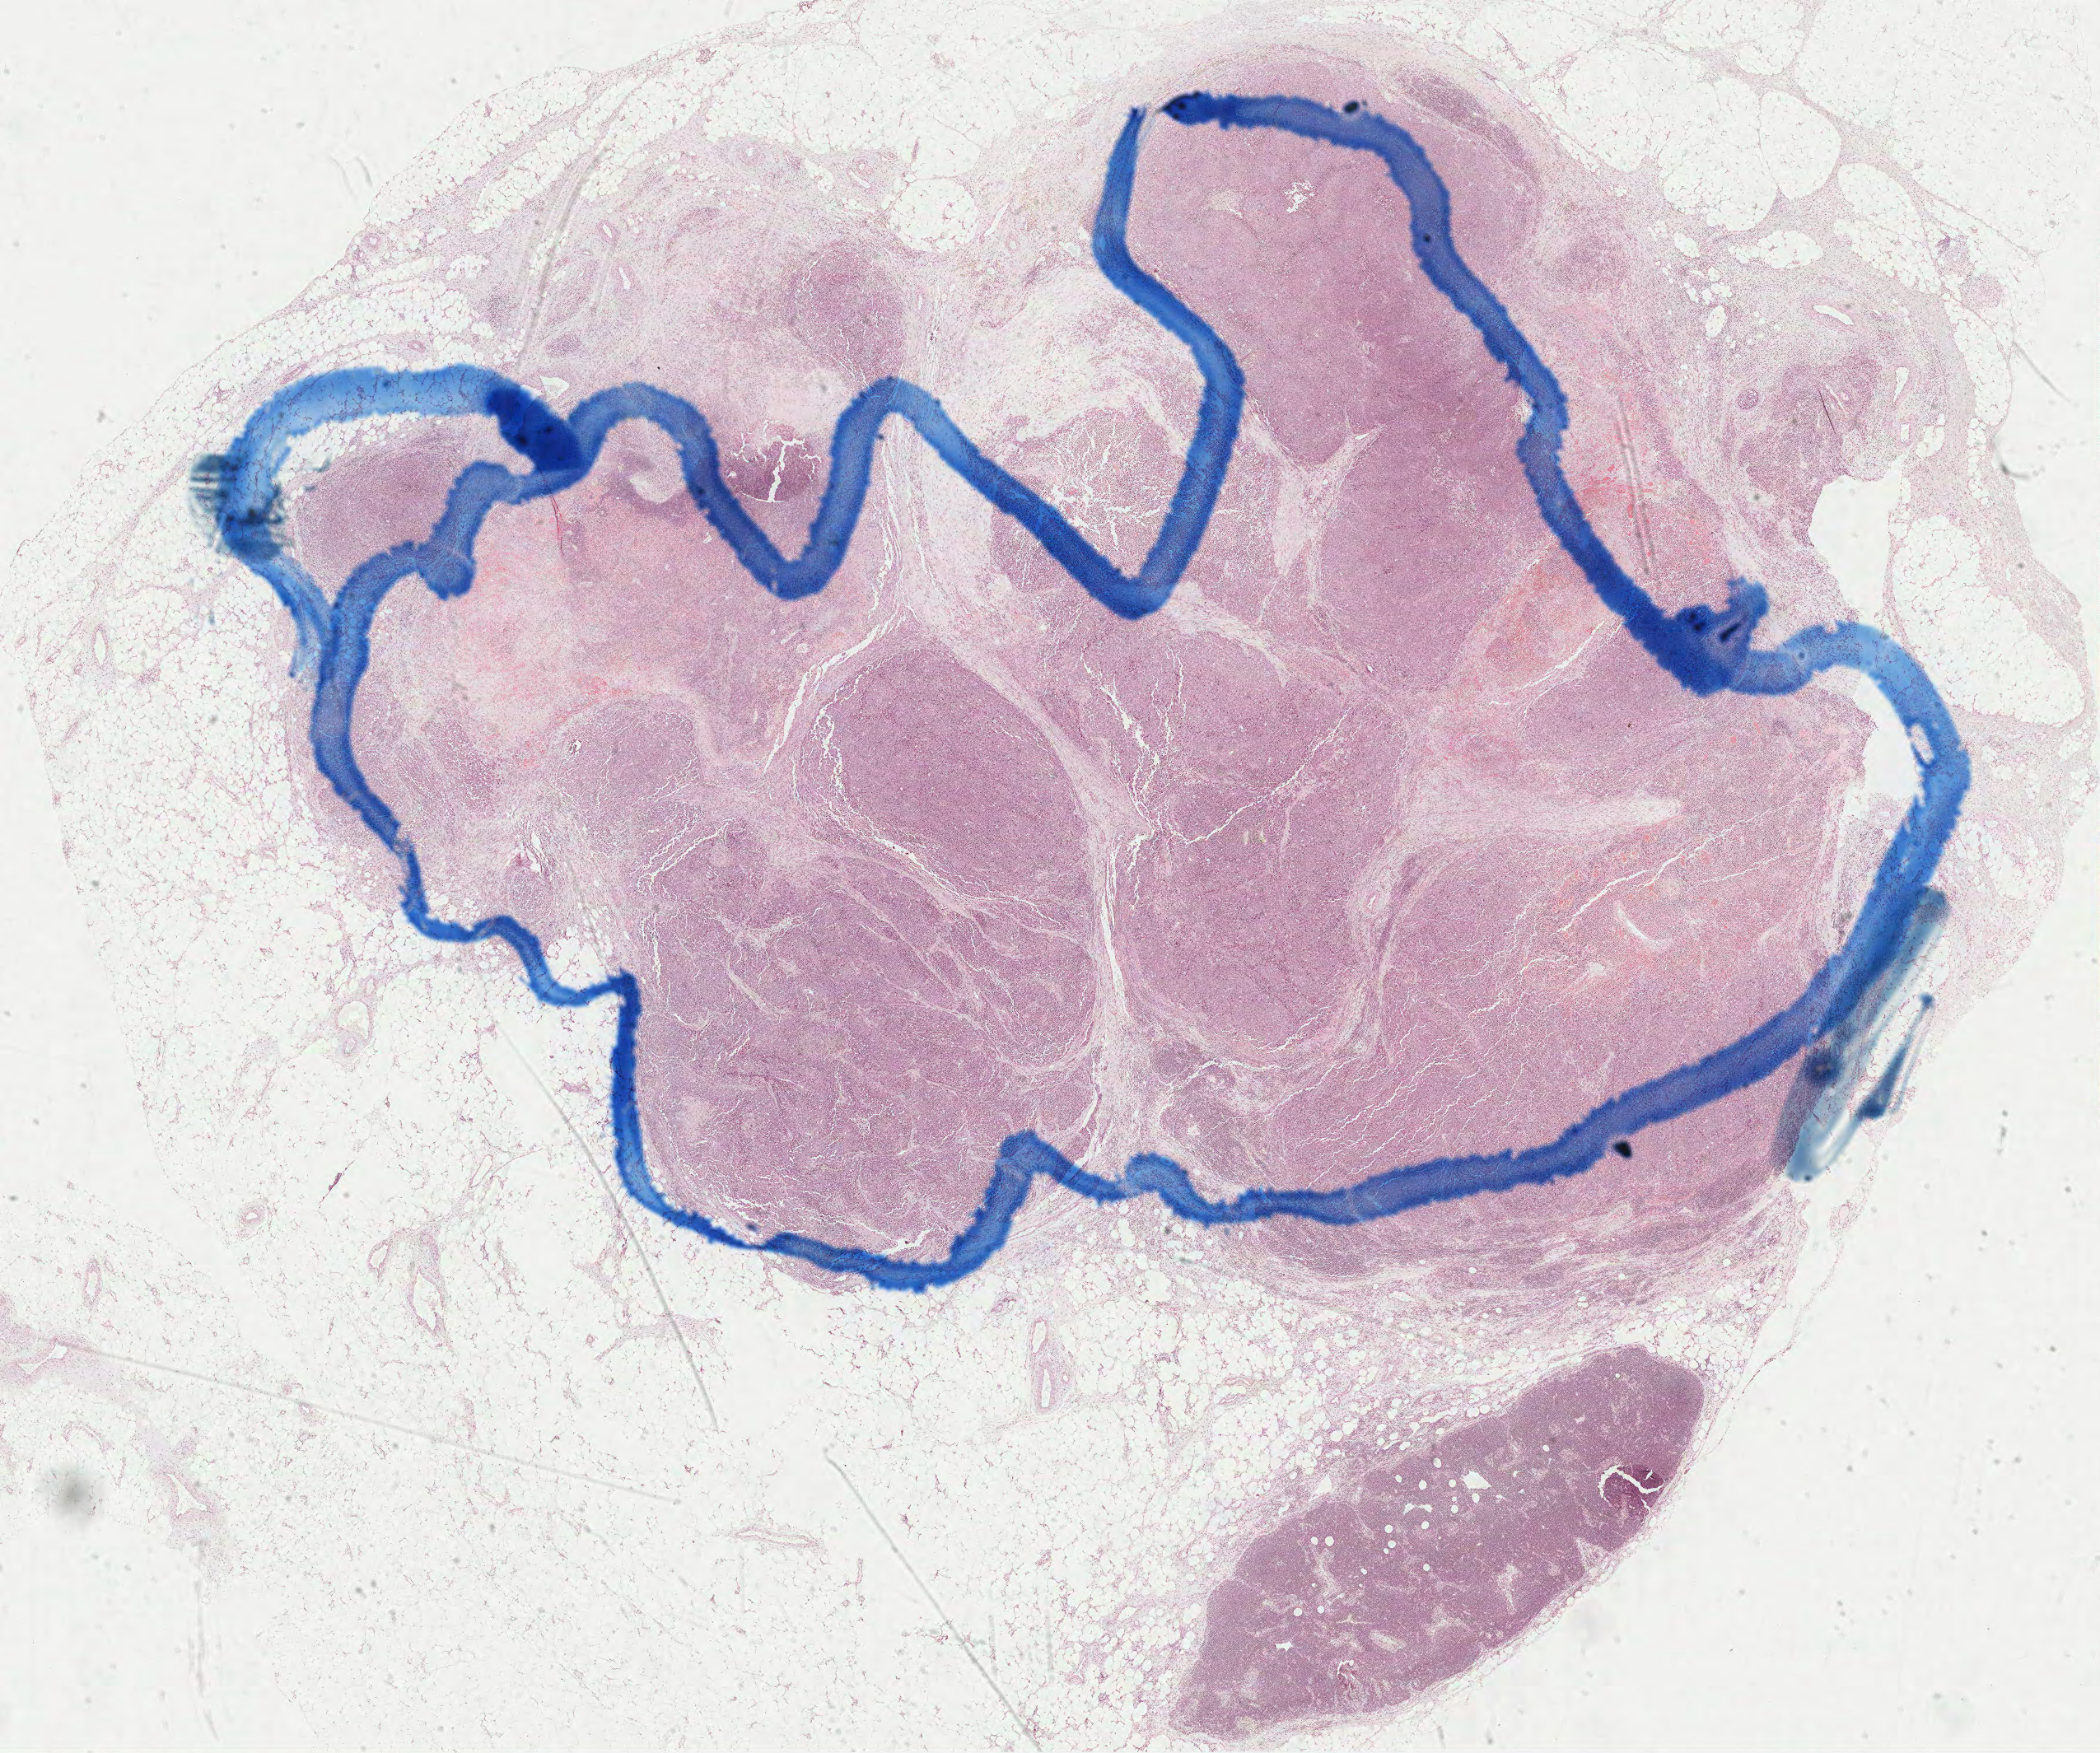
H&E whole-slide image — whole scanned area (about 20.4 x 17.1 mm) shown as a low-resolution overview; formalin-fixed paraffin-embedded (FFPE) diagnostic section; metastatic tumour sample, sampled site not recorded. Female, age 75 years at initial diagnosis.
This section: metastatic tumour tissue. Patient diagnosis: Malignant melanoma, NOS.